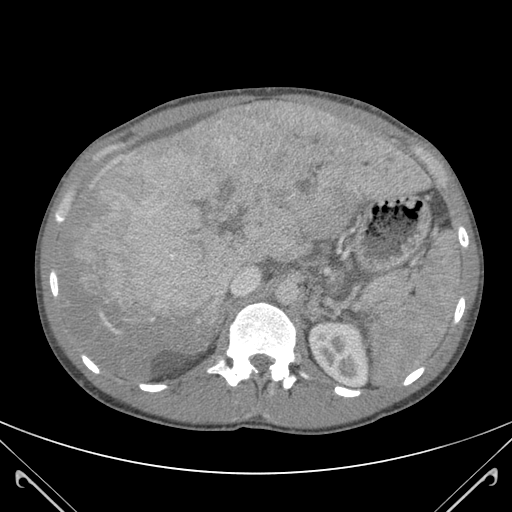
Contrast-enhanced abdominal CT (liver protocol), one axial slice. 120 kVp. Soft-tissue window (W 400 / L 40 HU). 512 × 512 image matrix, field of view 380 × 380 mm. From the clinical record (not read from this slice): diagnosis: hepatocellular carcinoma (patient treated with transarterial chemoembolisation; whether this scan precedes or follows treatment is not stated here); TNM stage (as recorded): Stage-IIIB; Child-Pugh class: A; tumour nodularity: uninodular.
Outlined on this slice (semi-automatic segmentation, software-assisted and operator-edited):
- abdominal aorta: bounding box (x1, y1, x2, y2) in pixels: (275, 281, 298, 306)
- liver parenchyma outside the tumour (the mass and vessels are separate outlines, so this box may not span the whole liver): (58, 105, 423, 378)
- mass: (71, 106, 426, 348)
- liver vessels: (100, 107, 289, 324)